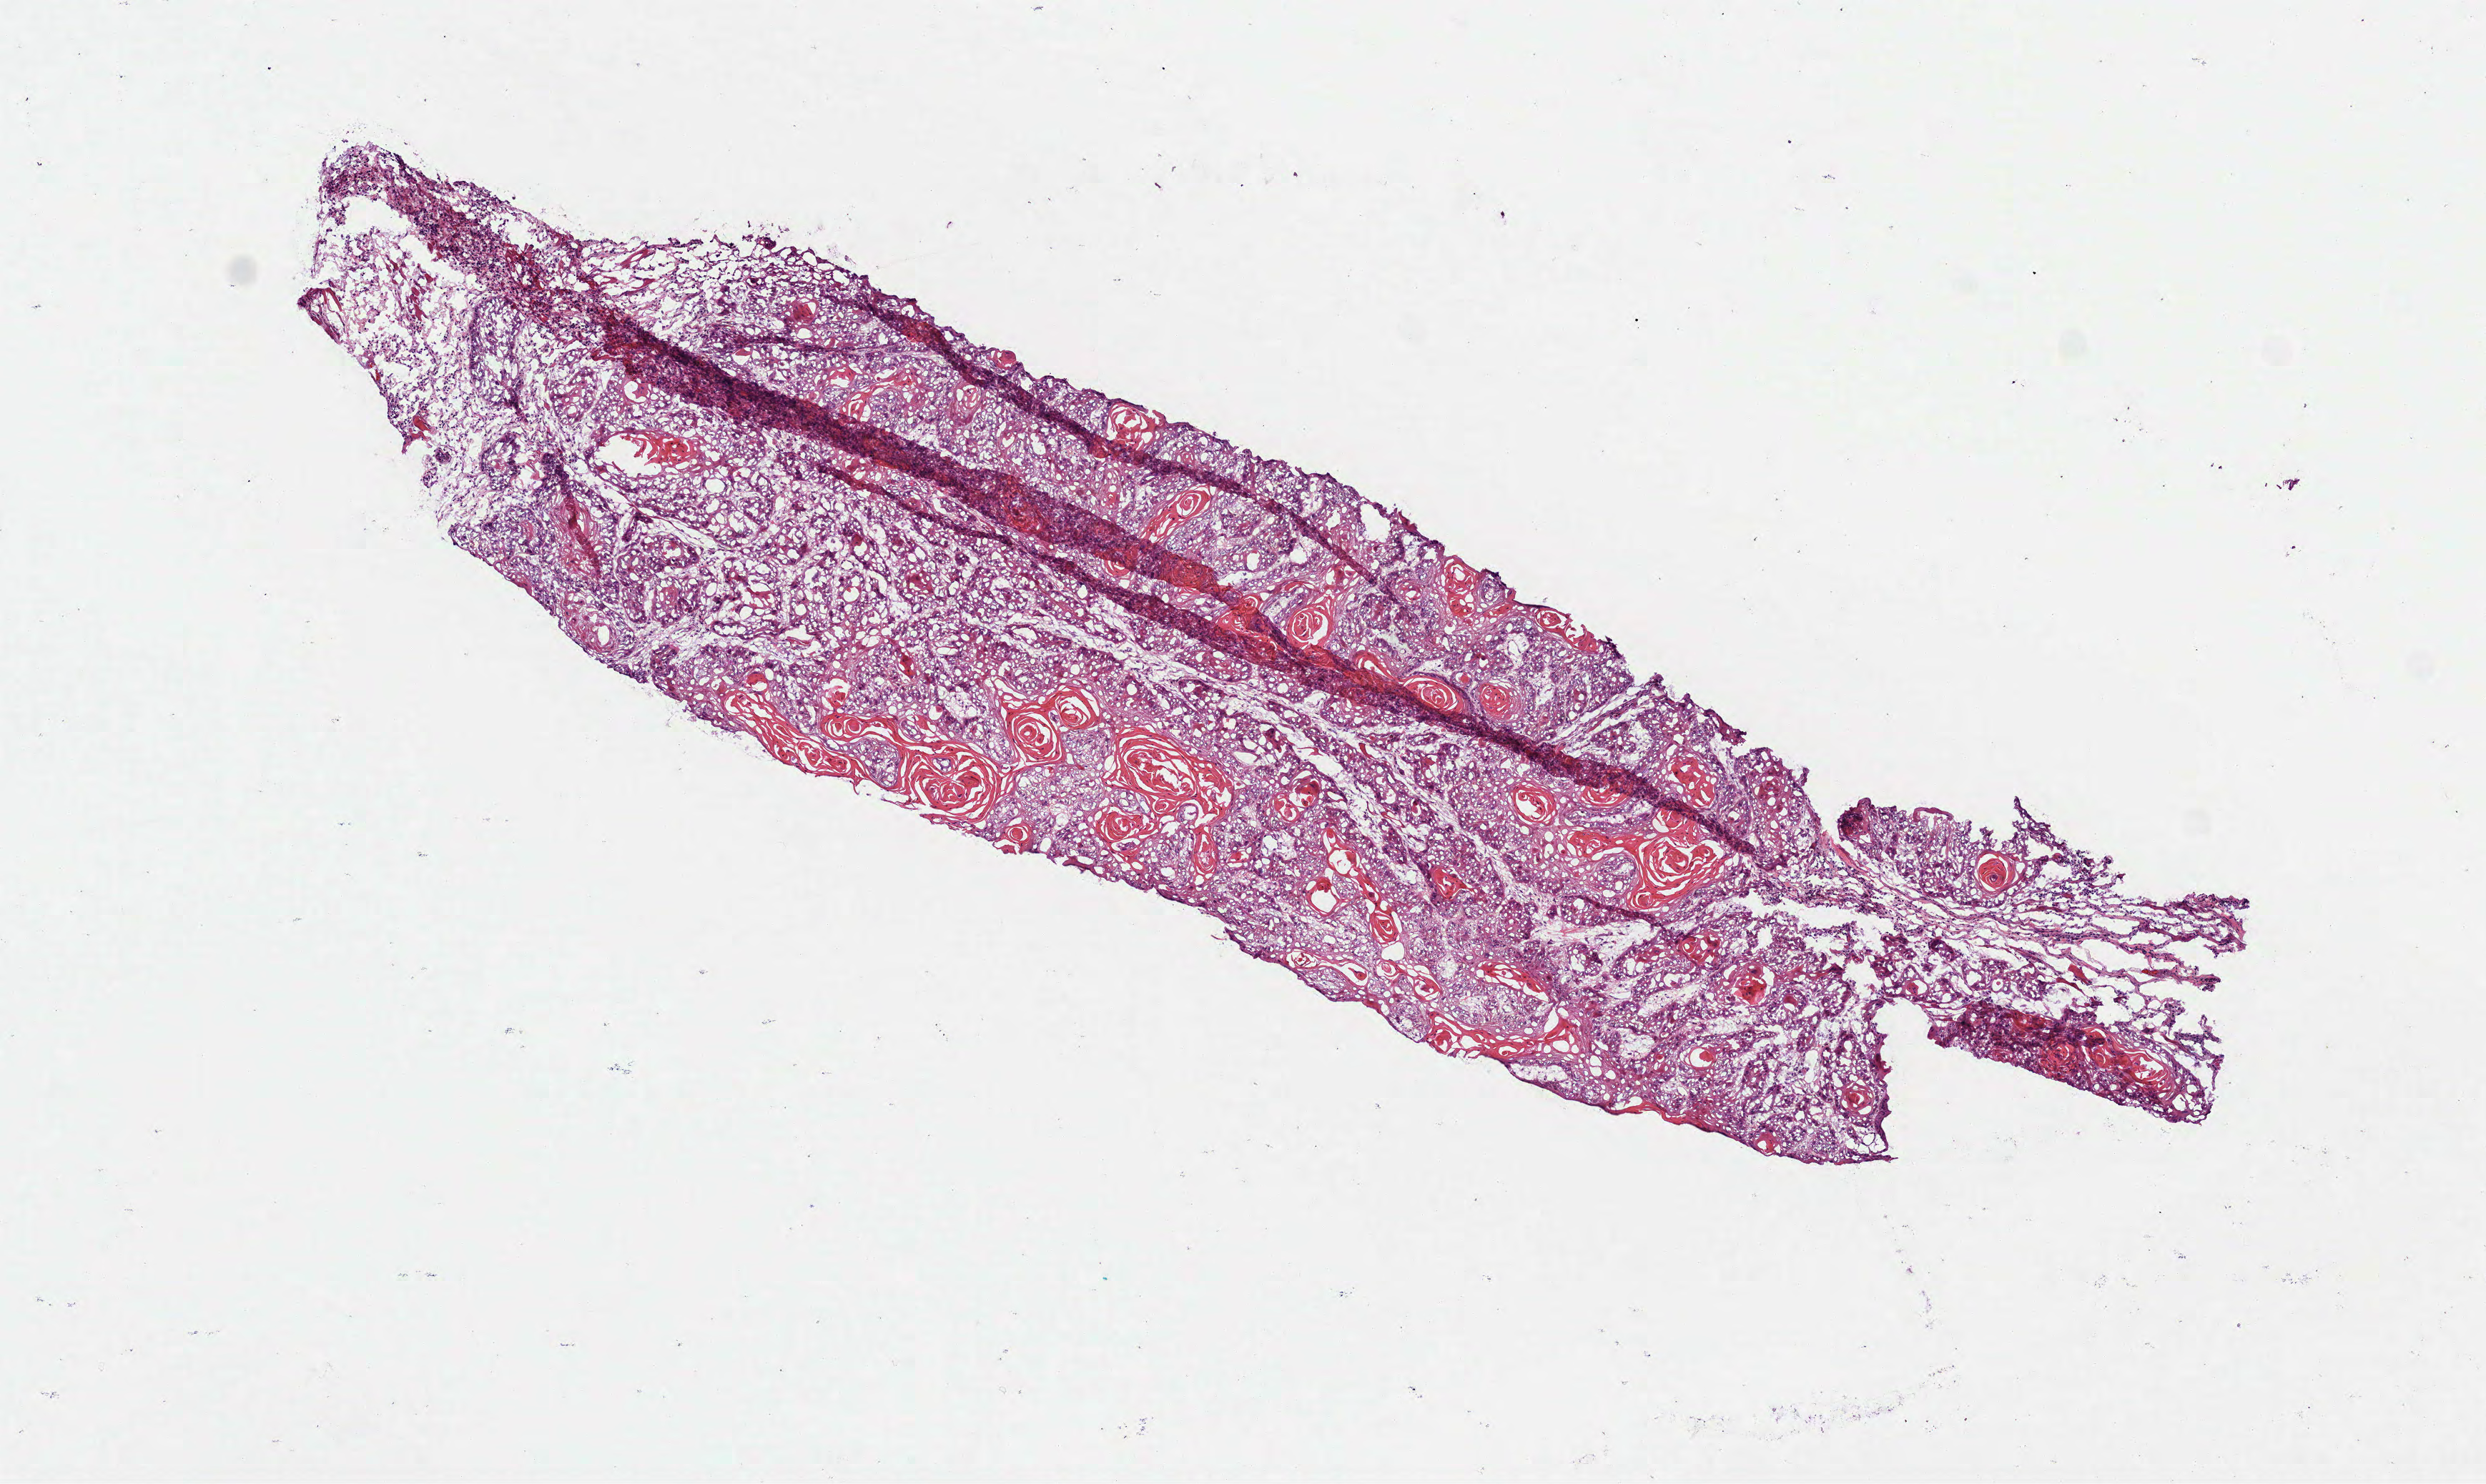
Digitized H&E-stained tissue section (whole slide) — a low-resolution overview of the entire scanned area, about 7.0 x 4.2 mm (slide scanned at 40x); frozen section from the top of the tissue portion; primary tumour sample from the head and neck. Male, age 40 years at initial diagnosis. Histologic grade: G2 (moderately differentiated). Composition of this section per pathologist review: tumour cells 100%, tumour nuclei 80%, normal cells 0%, stromal cells 0%, necrosis 0%. Infiltration values recorded for this section: lymphocyte infiltration 5%, monocyte infiltration 0%, neutrophil infiltration 0%.
AJCC pathologic stage: II (6th edition). Pathologic diagnosis: Squamous cell carcinoma, NOS (tongue, NOS).